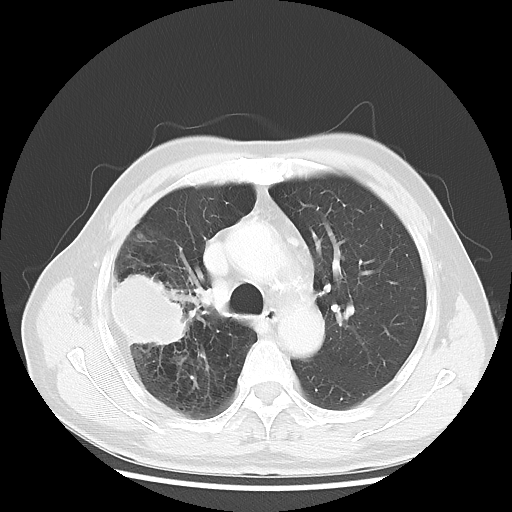
Chest CT, one axial slice; reconstruction kernel LUNG; lung window (W 1500 / L -600 HU); 5 mm slice thickness; 512 × 512 image matrix. Male patient, age 69 years. Case-level facts recorded for this patient, not image findings: clinical TNM (as recorded): T3 N0 M0; histopathological grade: G3.
Structures marked on this image (rectangle marked by the reading radiologist):
- lung tumour (recorded histology: adenocarcinoma): box from (x=107, y=273) to (x=189, y=353) px